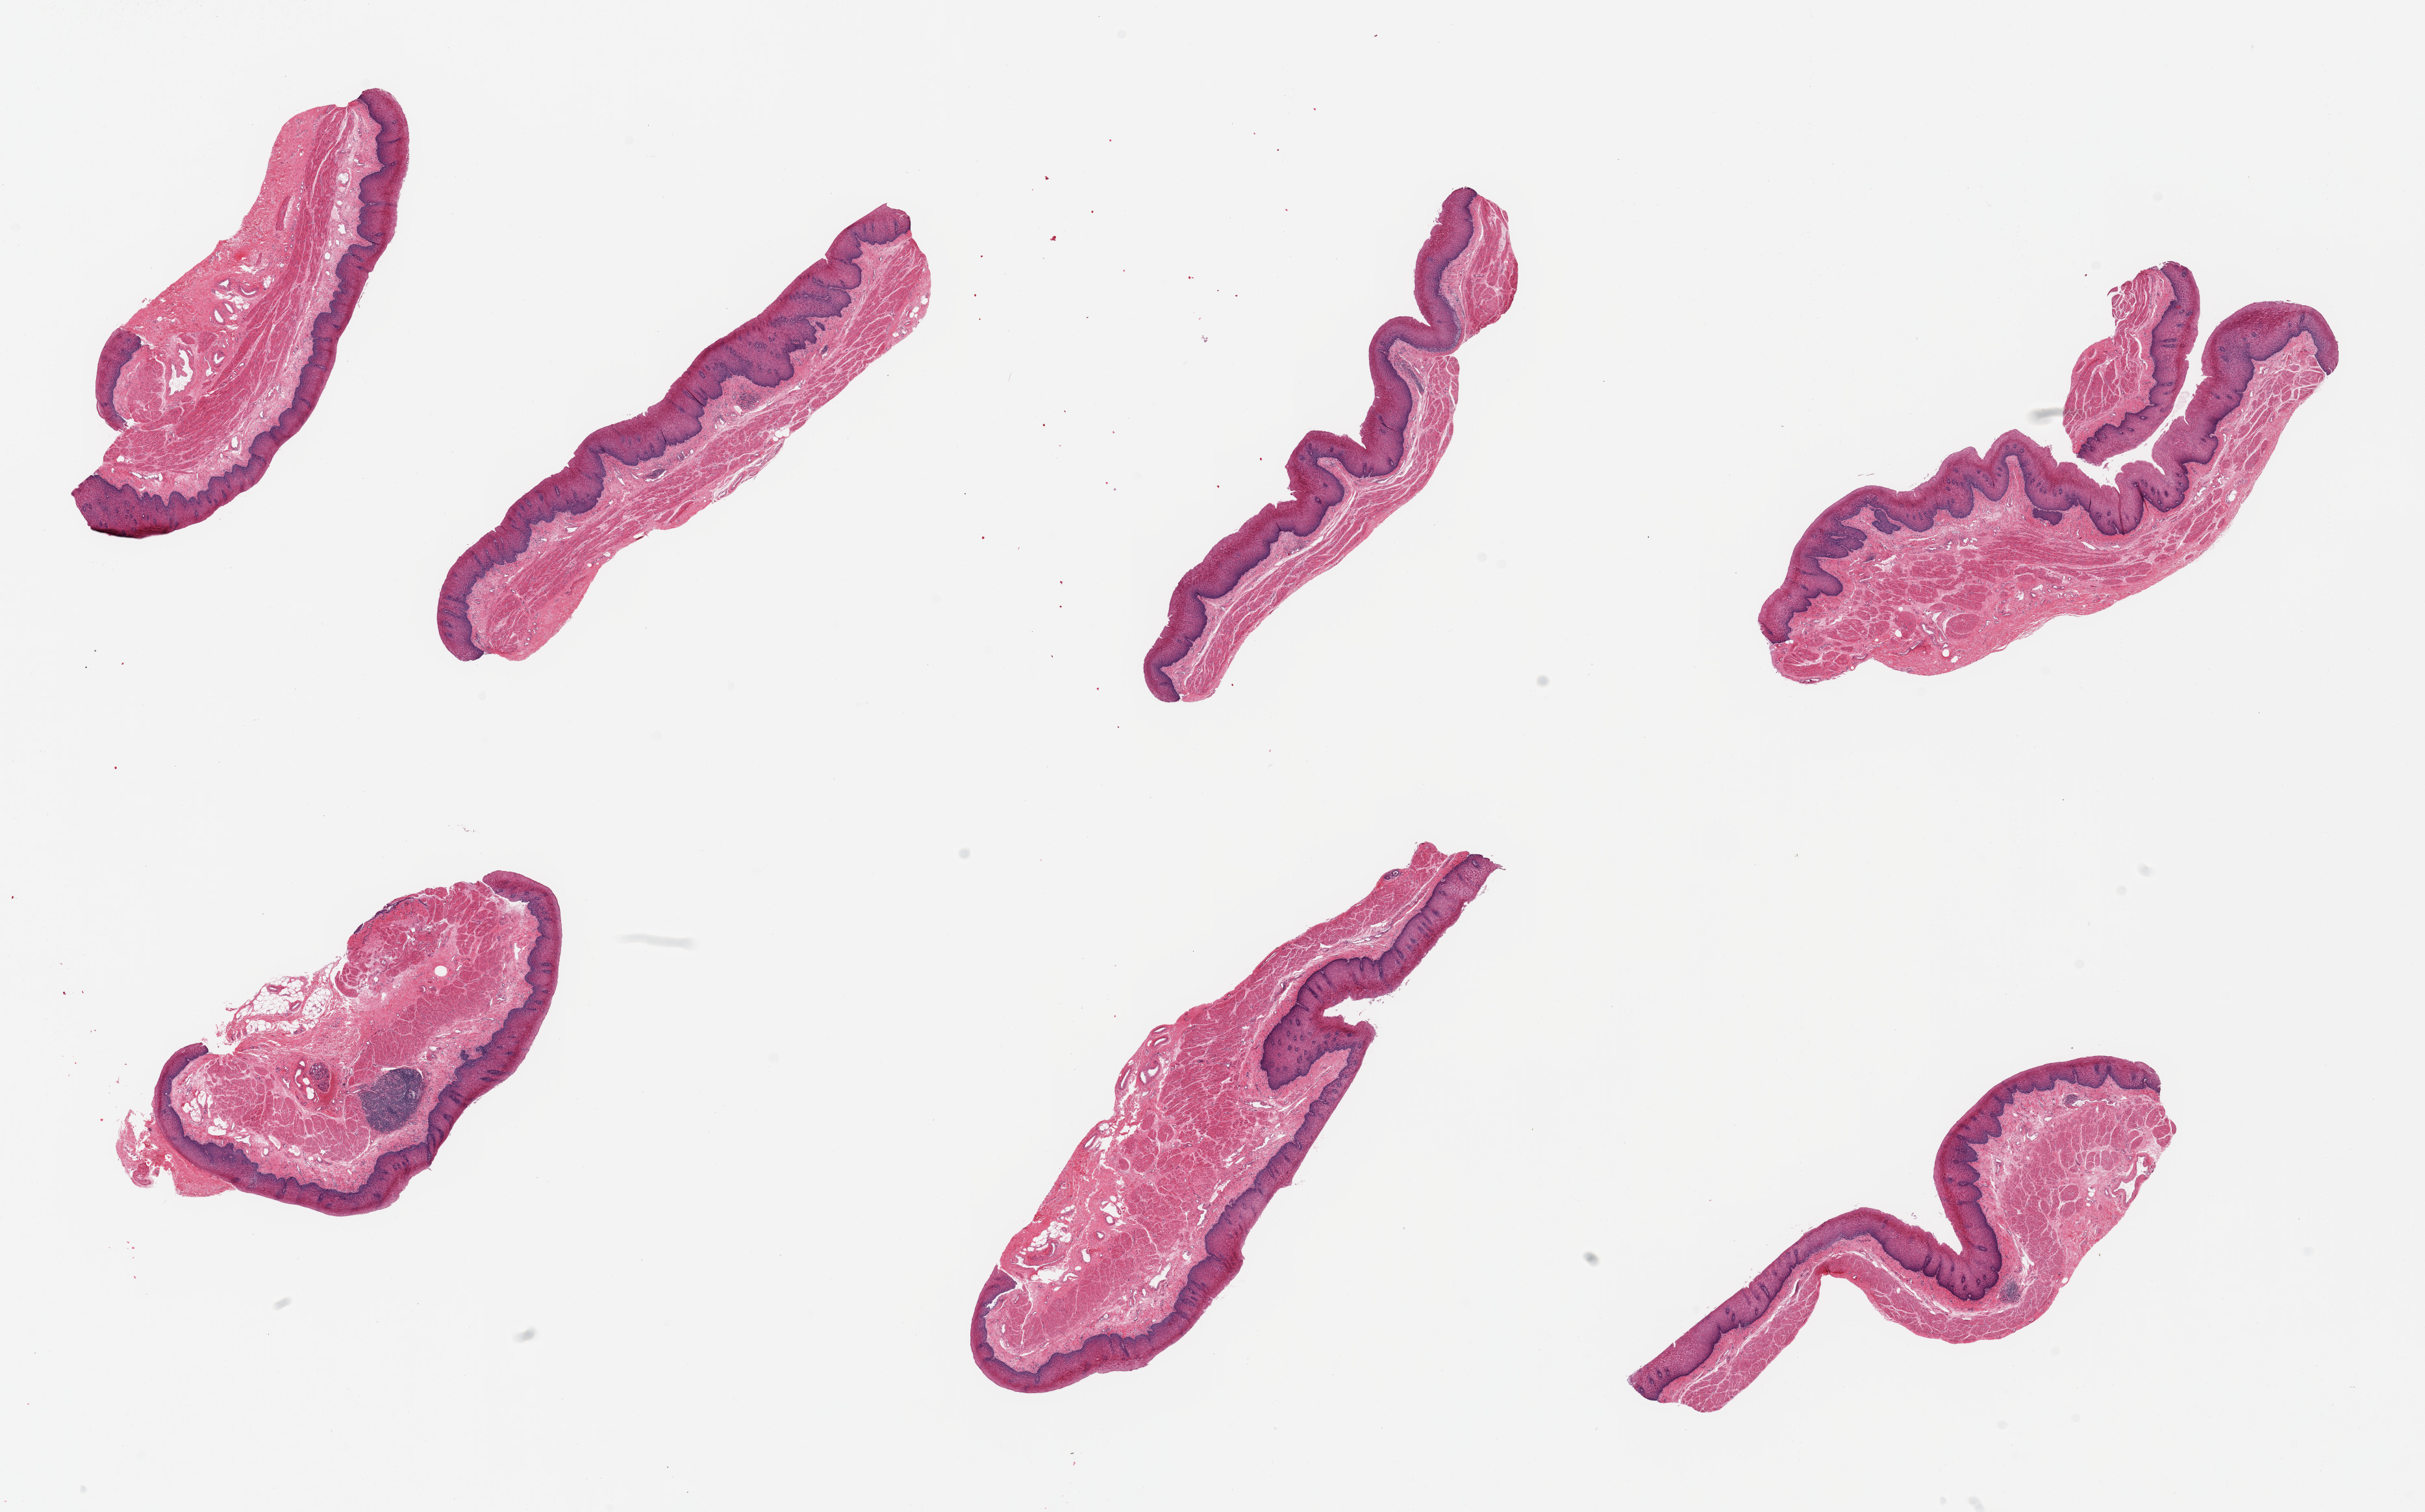
Whole-slide image, H&E stain — low-resolution overview of the scanned area, about 29.5 x 18.4 mm, PAXgene-fixed, paraffin-embedded tissue, section of esophageal mucous membrane (target tissue), tissue donor sample. Donor: male.
Pathologist's review note for this sample: 7 pieces; well dissected.